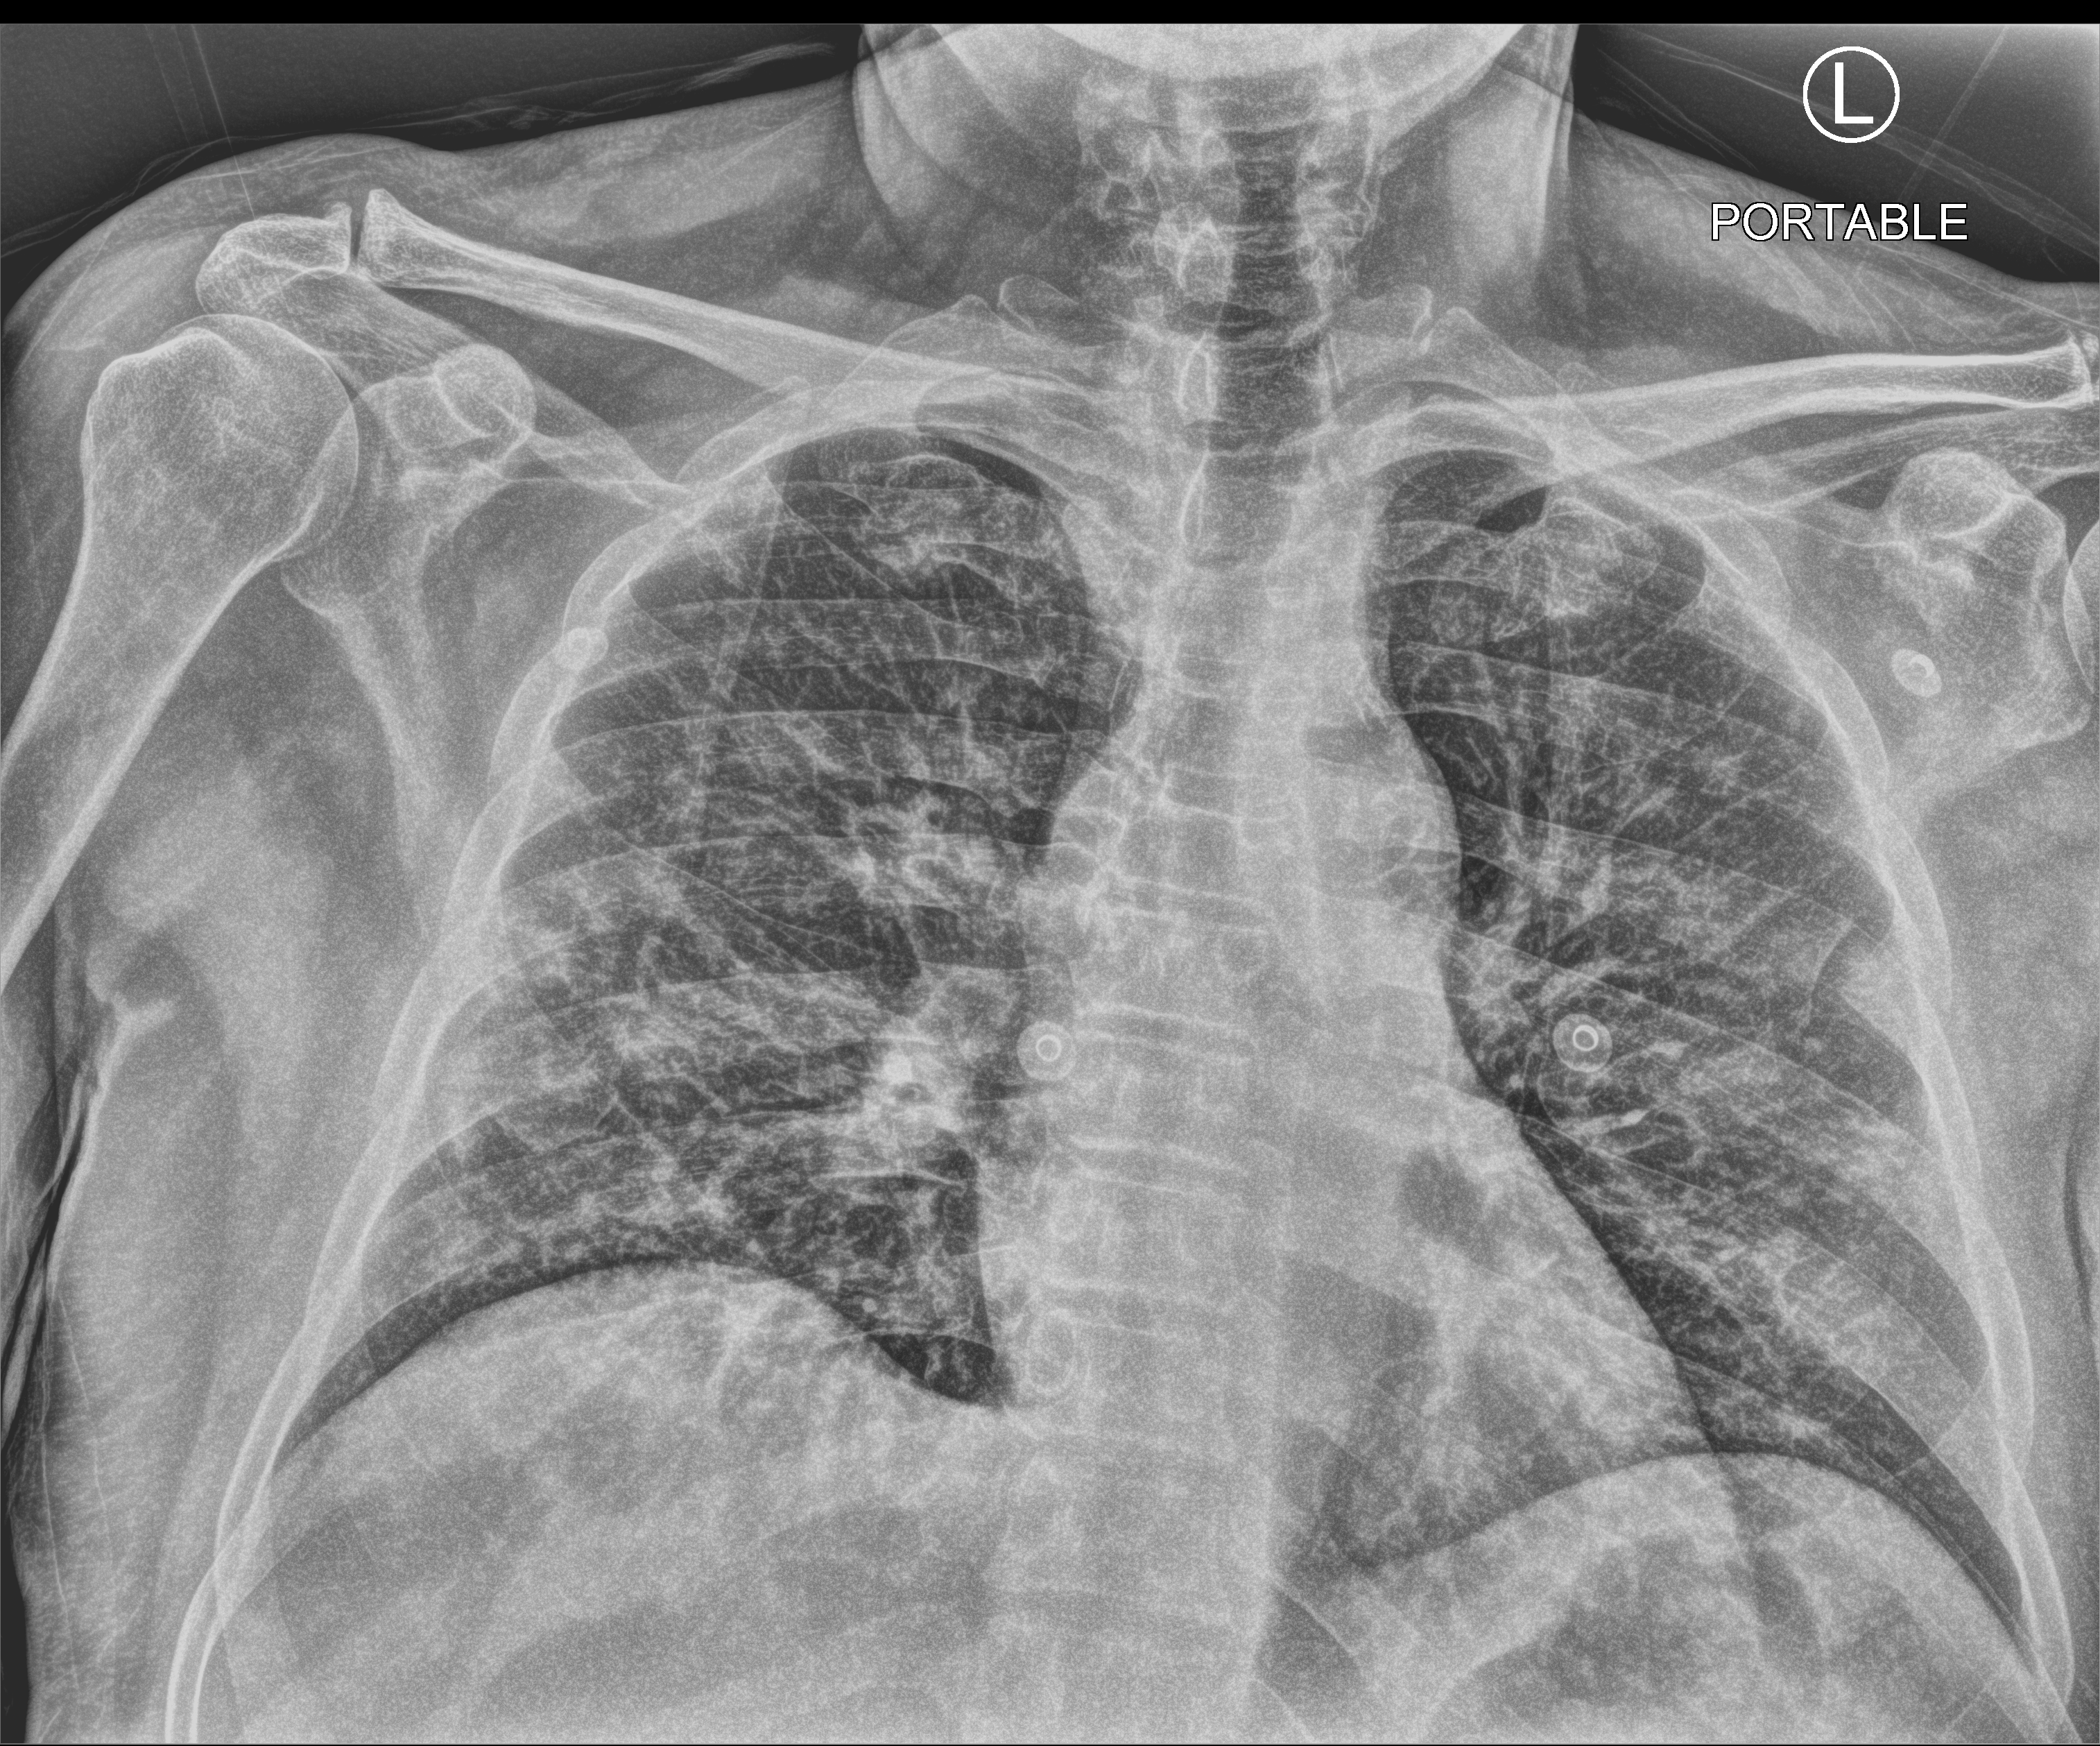
Chest X-ray (portable), anteroposterior (AP) projection. Patient hospitalised with COVID-19; male, aged 60–74 years.
From the hospital-stay record, not from the radiograph (when in the stay this image was taken is not recorded): length of hospital stay: 1 day; mechanically ventilated during this hospital stay: no.